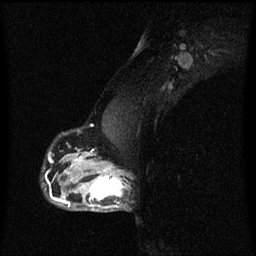
Breast MRI (dynamic contrast-enhanced), one sagittal slice; position 41 of 60 along the scan axis; dynamic contrast-enhanced series, image 2 of 3 at this slice position (ordered by acquisition); 1.5 T; TE 4.2 ms, TR 8.4 ms; 2 mm slice thickness; 256 × 256 image matrix, field of view 200 × 200 mm. Female patient, age 40 years.
Outlined on this slice (semi-automatic segmentation, software-assisted and operator-edited):
- analysis volume of interest (the breast-tissue region the enhancement analysis was run in; not a lesion): box from (x=76, y=172) to (x=128, y=213) px
- tumour enhancement mask (voxels above the 70 % enhancement threshold inside the analysis volume of interest): (x=82, y=172)–(x=127, y=209)